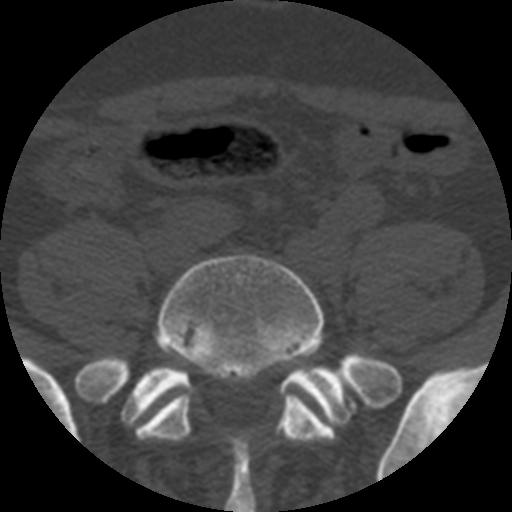
CT including the spine, one axial slice; position 55 of 508 along the scan axis; reconstruction kernel STANDARD; bone window (W 1800 / L 400 HU); 1.25 mm slice thickness; 512 × 512 image matrix, field of view 160 × 160 mm. Patient age 57 years. From the clinical record (not read from this slice): primary cancer: prostate.
Structures marked on this image (semi-automatically segmented with operator editing):
- L5 vertebra: bounding box <135,254,390,443> (left, top, right, bottom; pixels)